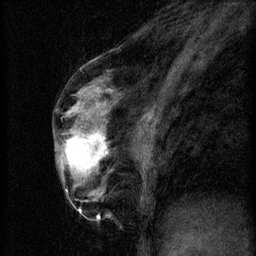
Breast MRI (dynamic contrast-enhanced), one sagittal slice. Position 28 of 60 along the scan axis. 3 images stored at this slice position (order not interpretable as contrast timing). 1.5 T. TE 4.2 ms, TR 8.2 ms. 256 × 256 image matrix, field of view 180 × 180 mm. Patient: female, 56 years.
Structures marked on this image (semi-automatic segmentation, software-assisted and operator-edited):
- analysis volume of interest (the breast-tissue region the enhancement analysis was run in; not a lesion): bounding box (x1, y1, x2, y2) in pixels: (60, 124, 113, 179)
- tumour enhancement mask (voxels above the 70 % enhancement threshold inside the analysis volume of interest): (65, 132, 106, 171)